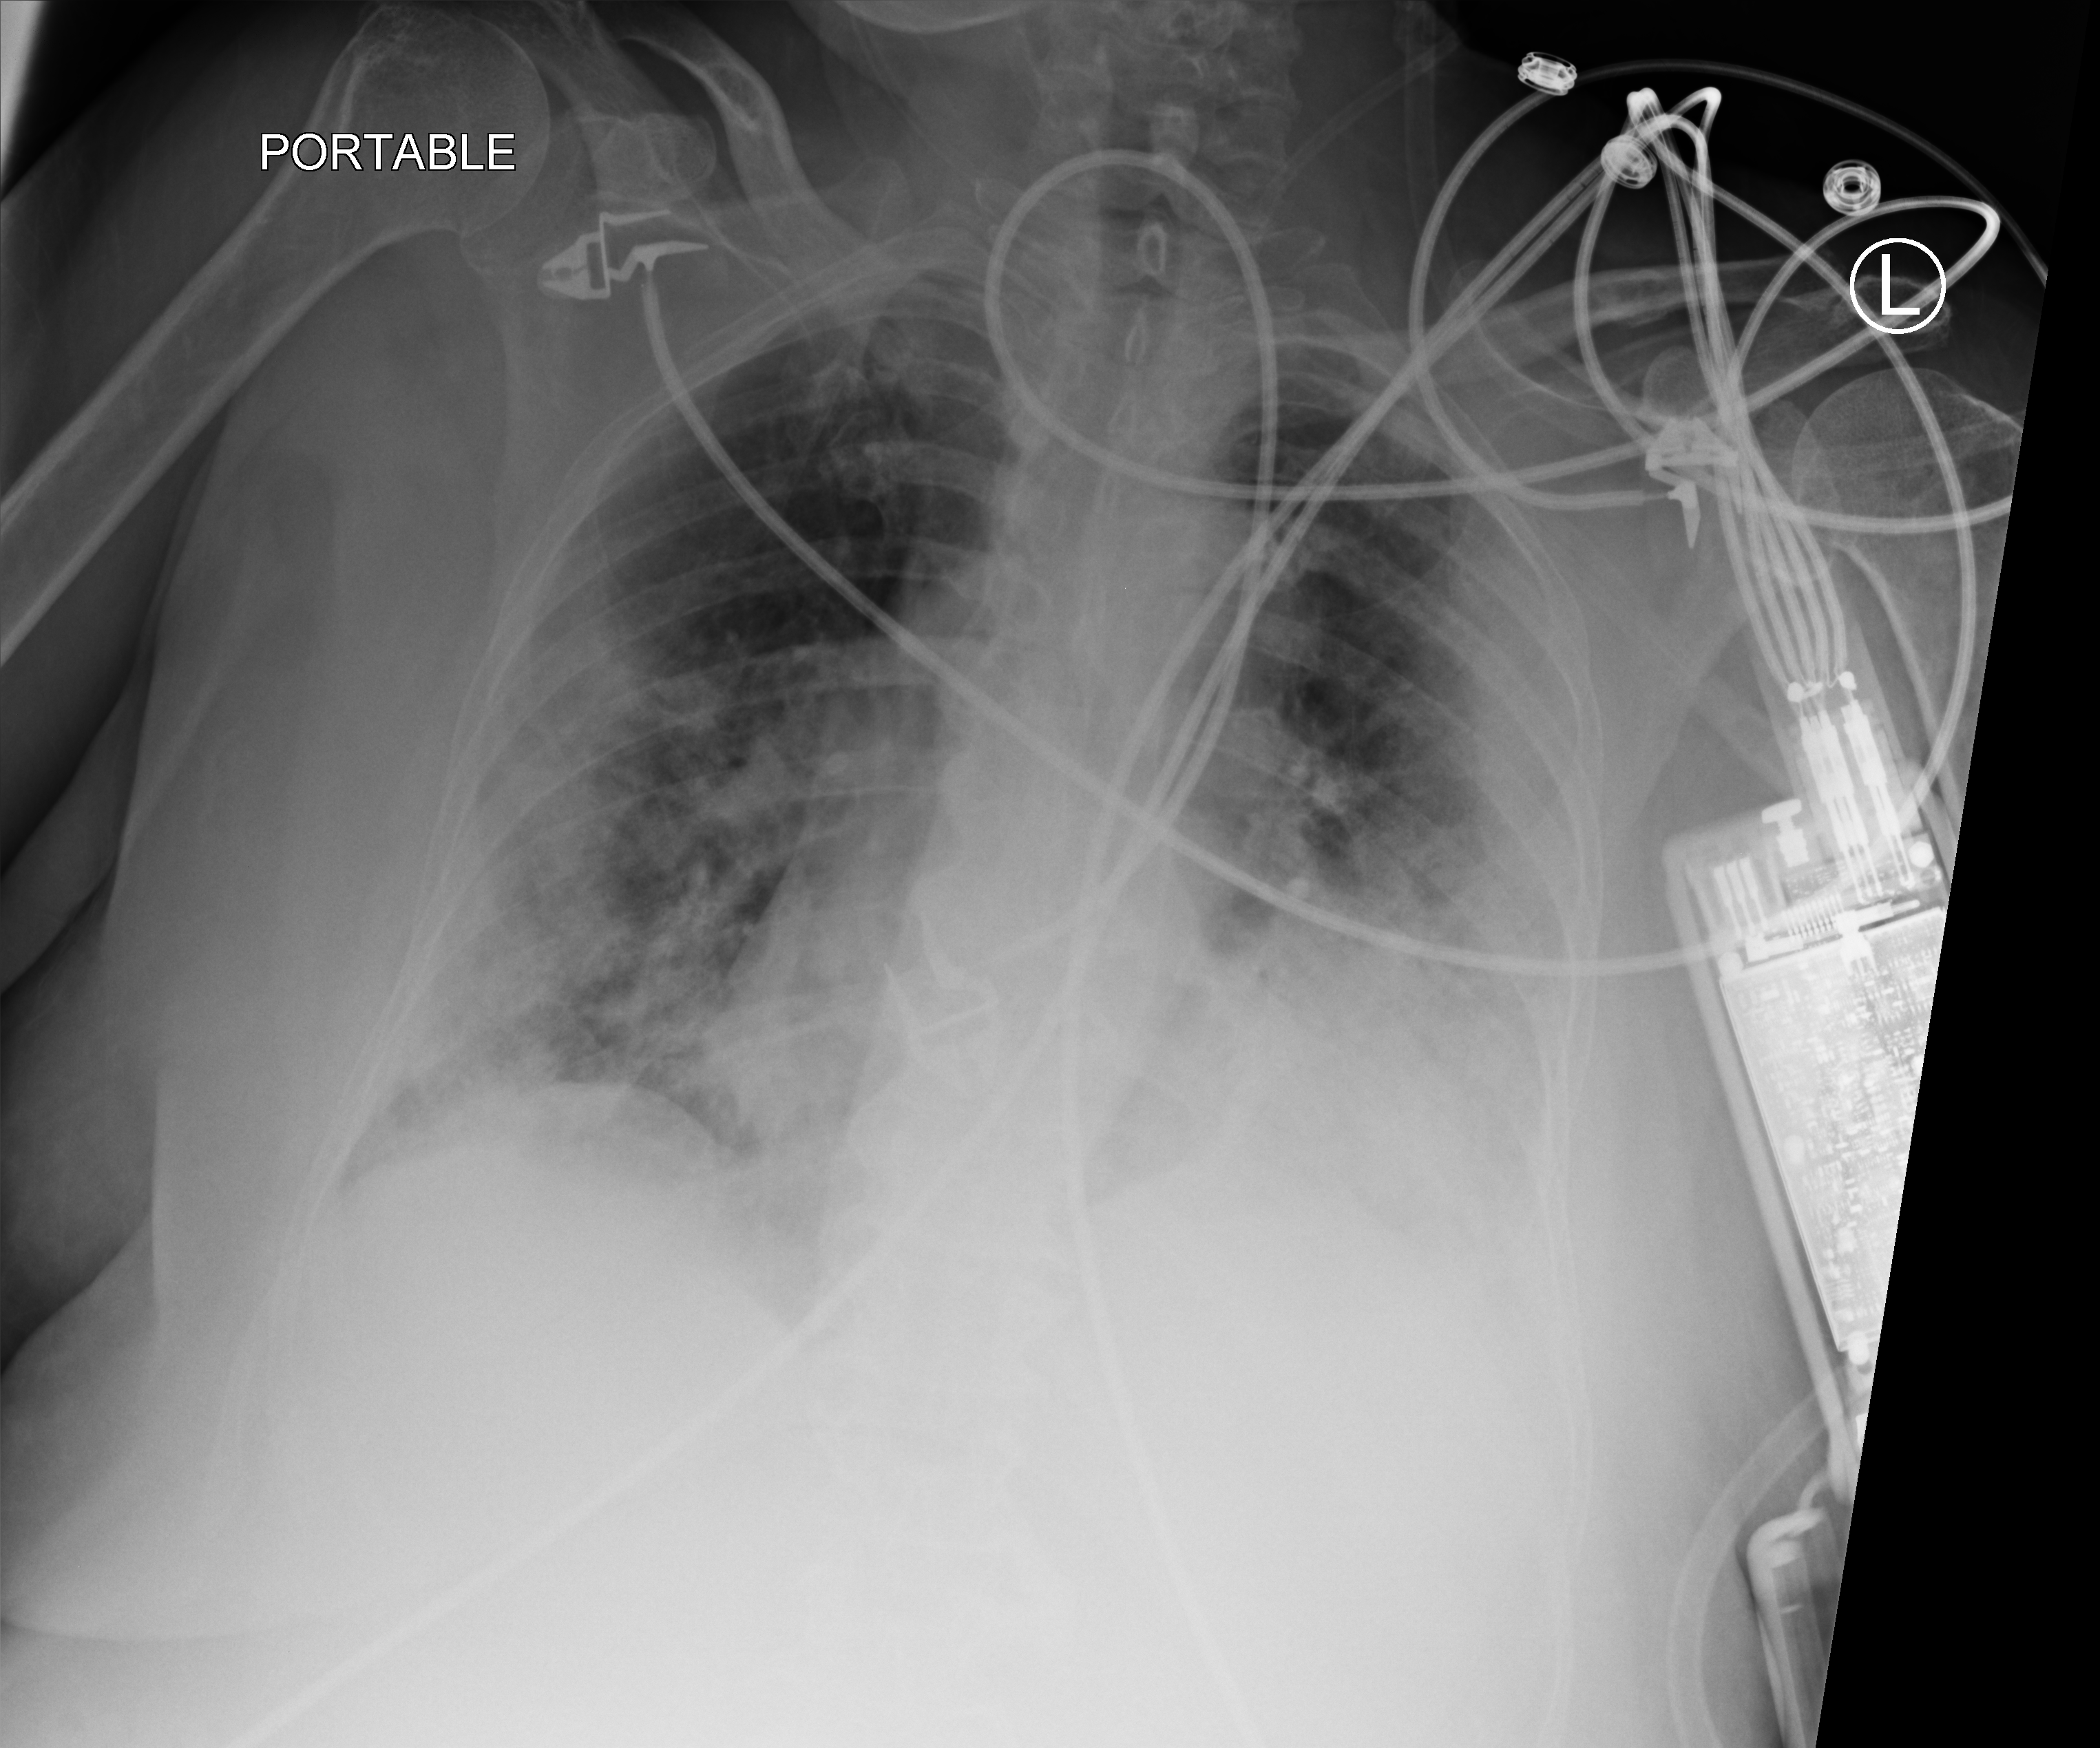
Portable chest radiograph; anteroposterior (AP) projection. Female patient hospitalised with COVID-19, age 75–90 years.
From the hospital-stay record, not from the radiograph (when in the stay this image was taken is not recorded): smoking status (admission record): former; admitted to intensive care during this hospital stay: yes.